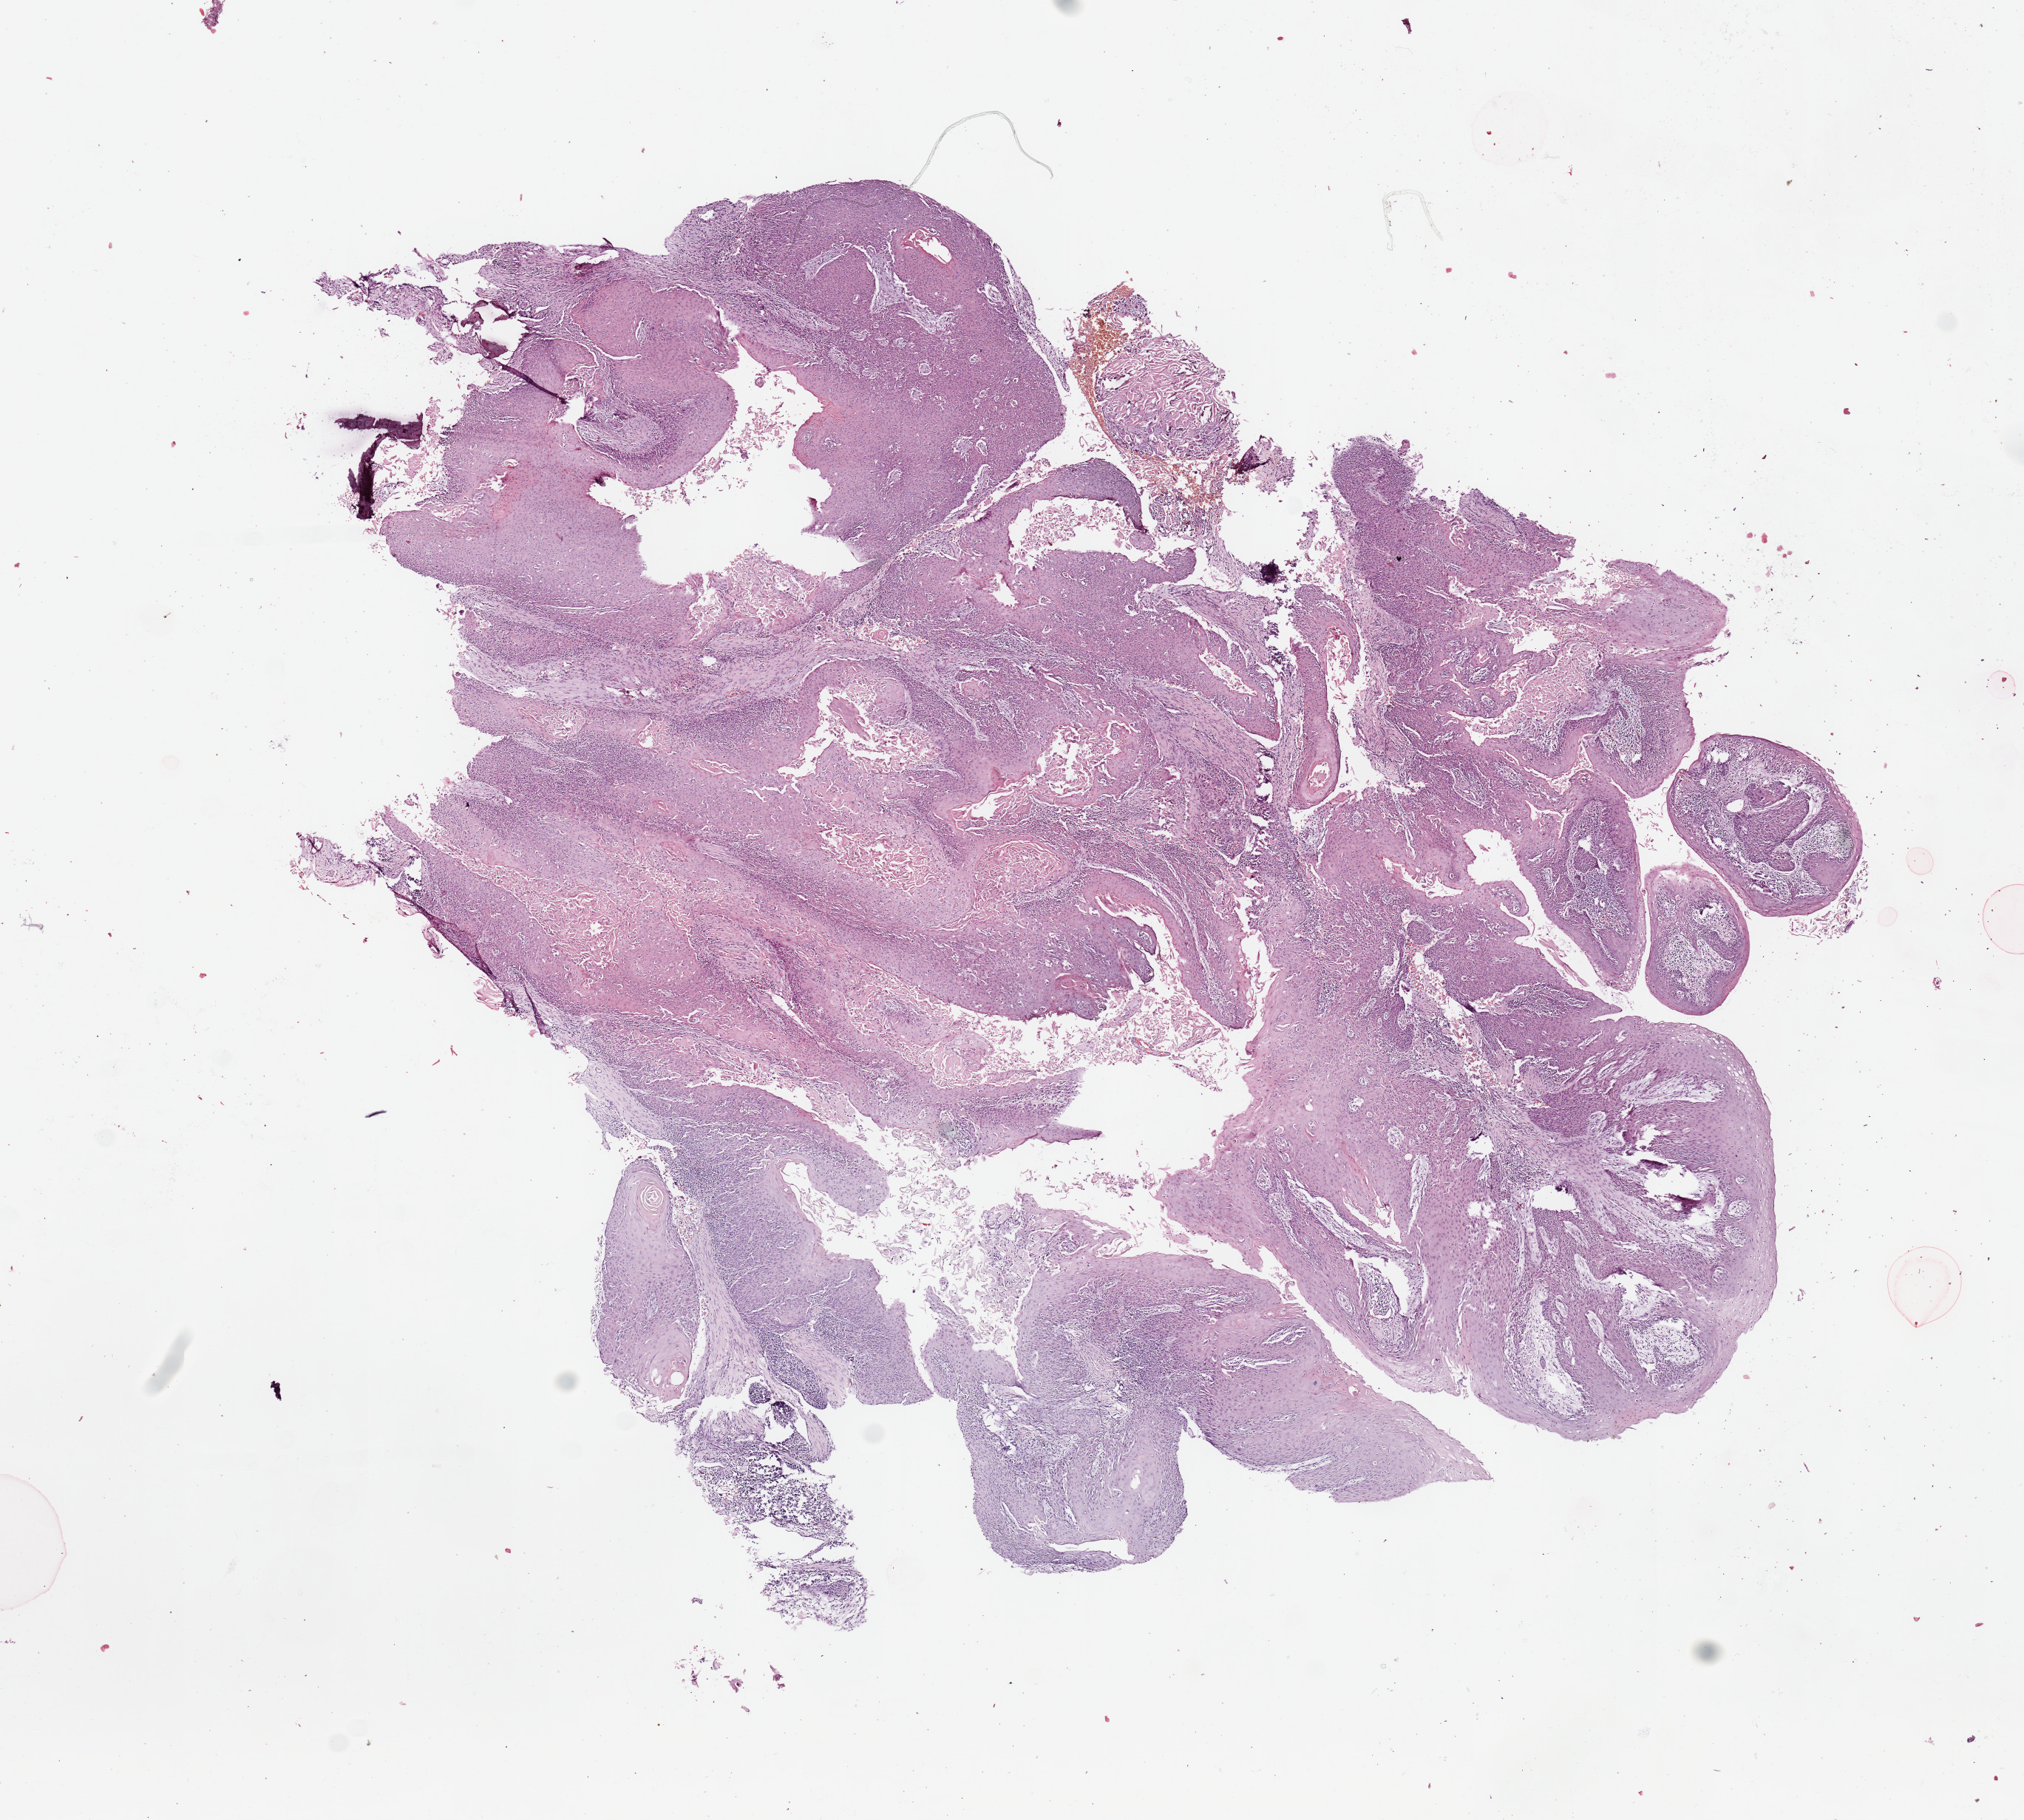
Whole-slide histology image, H&E-stained, low-resolution overview of the scanned area, about 10.8 x 9.7 mm. Tumour tissue sample, sampled site: alveolar ridge. Female, 53 y/o. Composition of this section per pathologist review: tumour nuclei 85%, necrosis 5%.
Histologic diagnosis: Squamous cell carcinoma, NOS (gum, NOS).